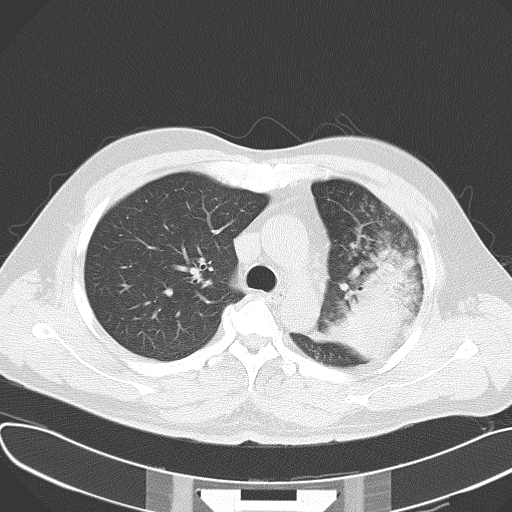
Chest CT, one axial slice. Slice 44 of 62 in the series (ordered by position). Reconstruction kernel B70f. 120 kVp. Lung window (W 1500 / L -600 HU). 512 × 512 image matrix. Male patient, age 48 years. Case-level facts recorded for this patient, not image findings: clinical TNM (as recorded): T4 N0 M0.
Structures marked on this image (bounding box drawn by a radiologist):
- lung tumour (recorded histology: adenocarcinoma): box from (x=324, y=255) to (x=410, y=363) px